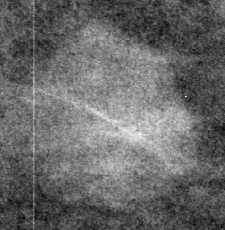
Region of interest cut from a scanned film mammogram (one marked finding); left breast; CC view.
- Mass, shape oval, margins circumscribed; BI-RADS assessment category 3; subtlety rating 5 on a 1 (subtle) to 5 (obvious) scale; pathology result (as recorded, not read from the image): benign.